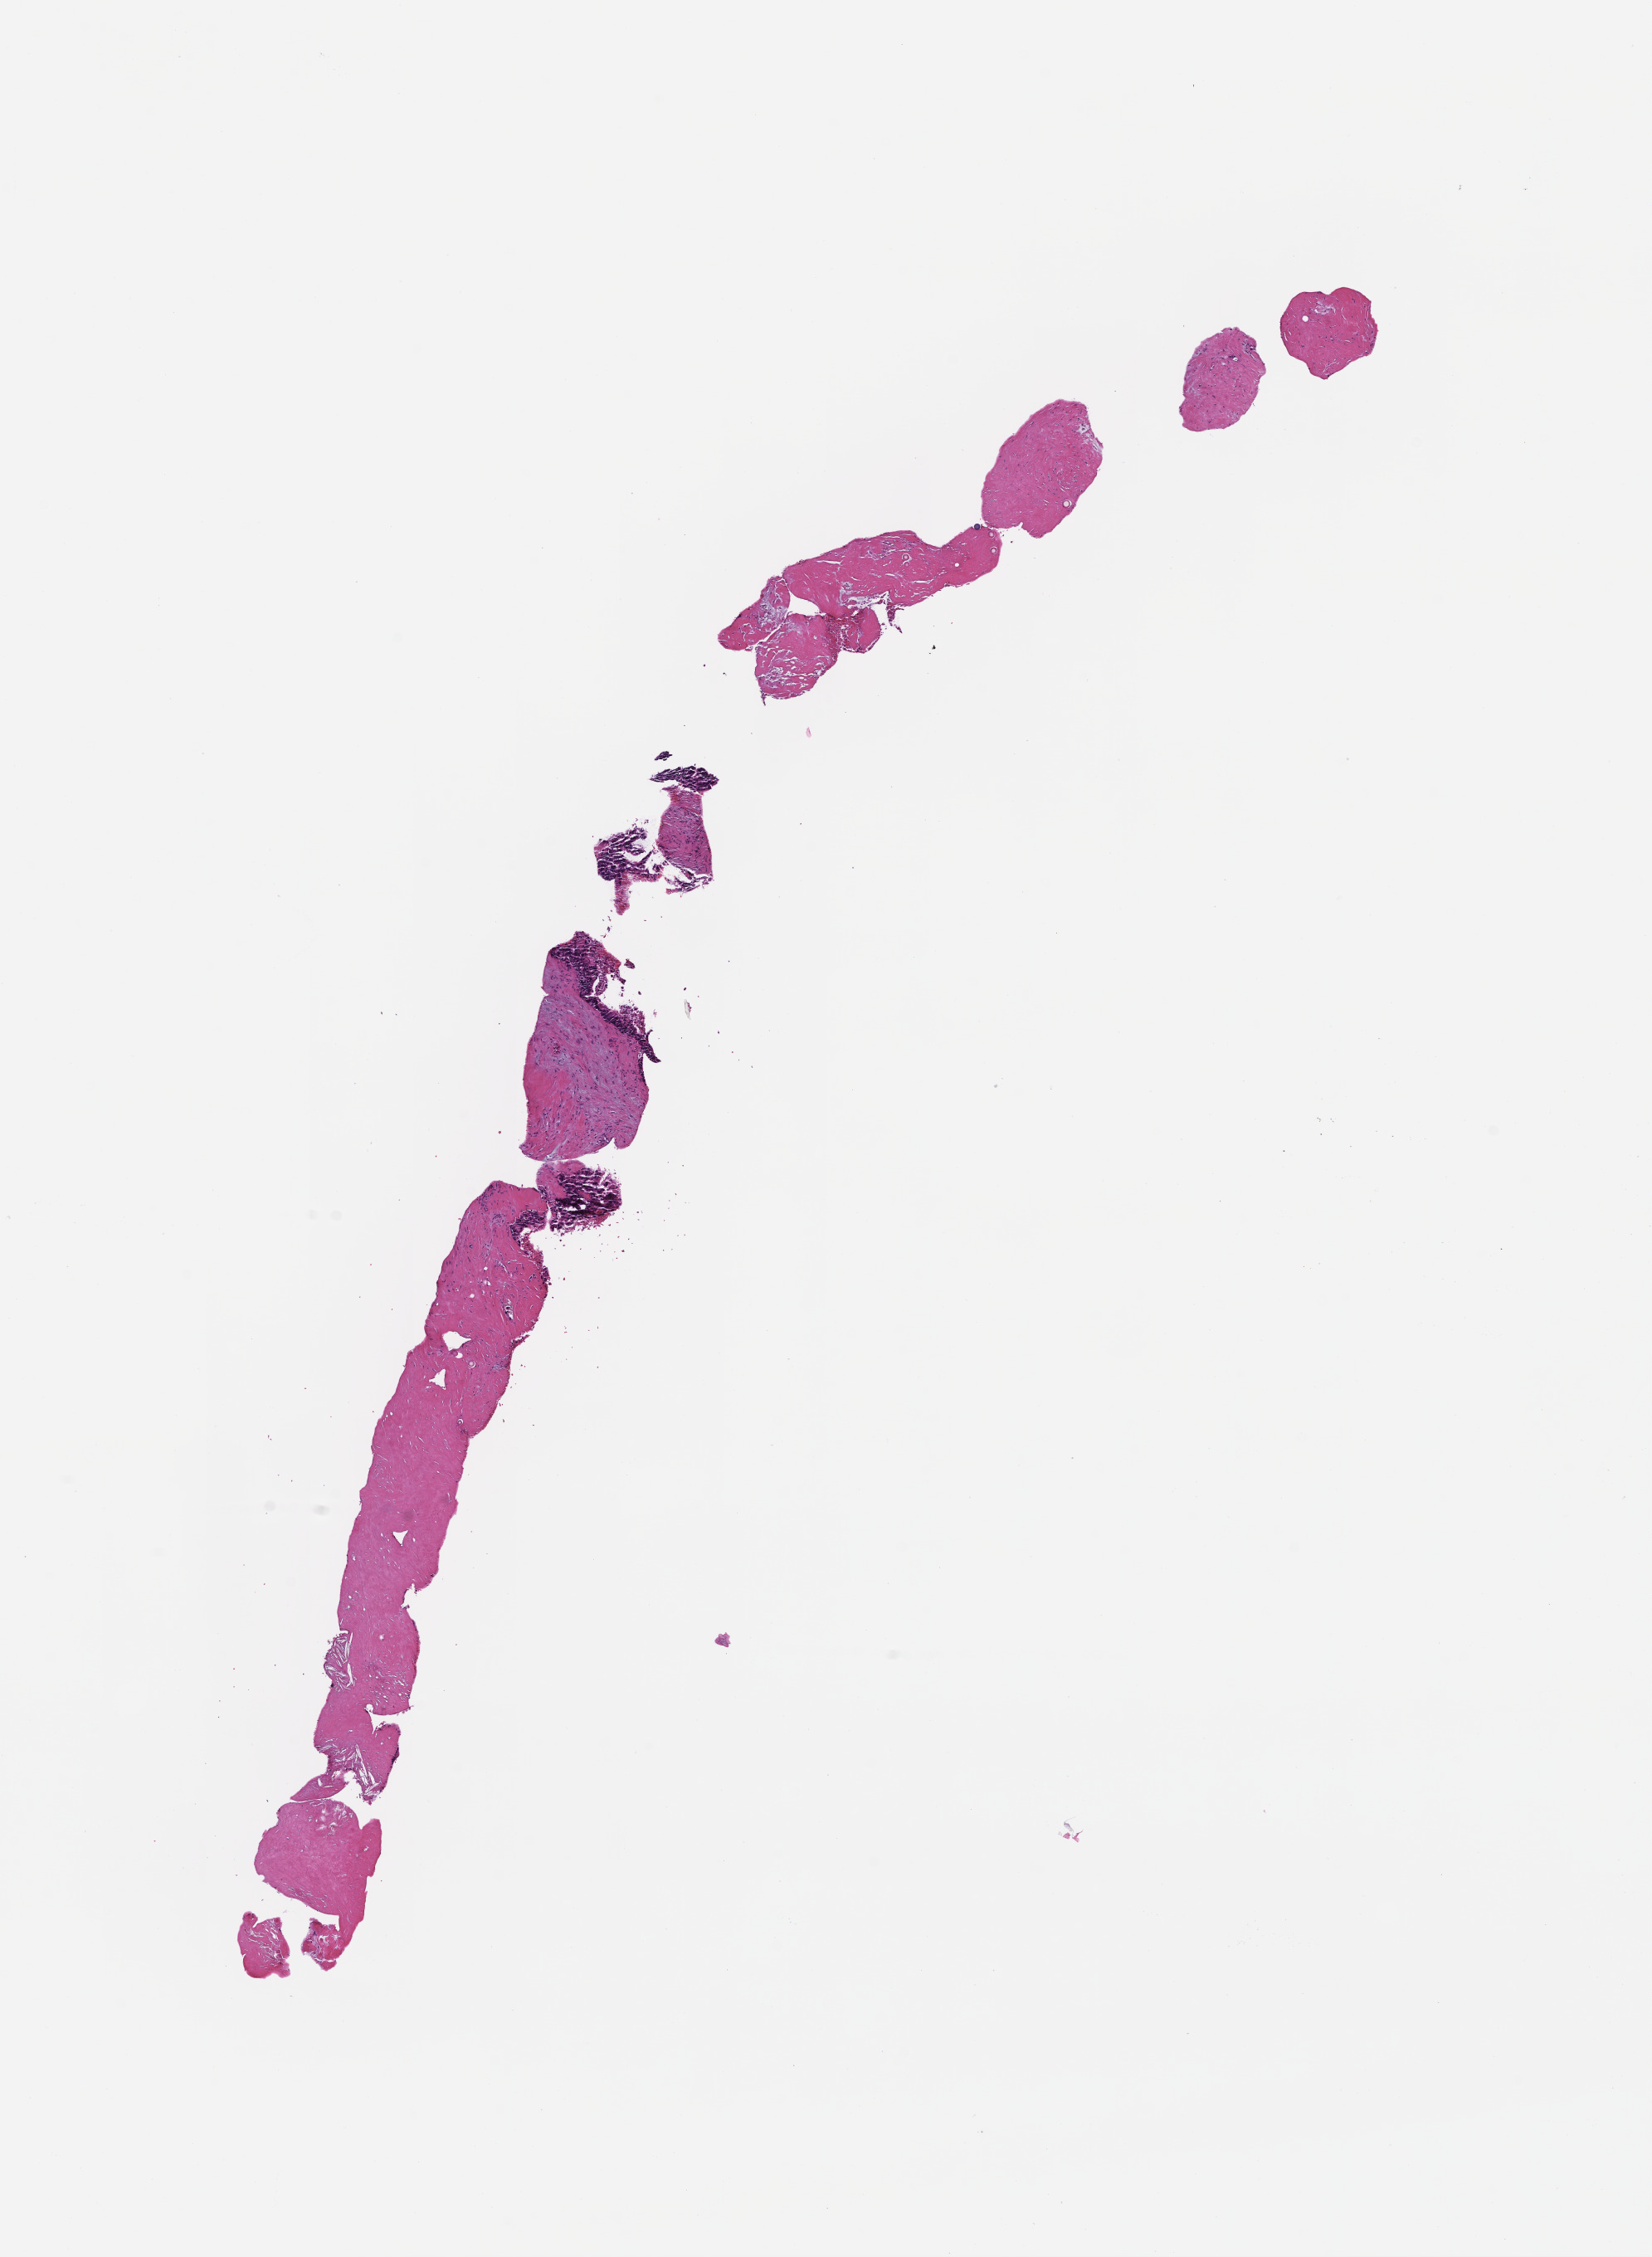
Hematoxylin and eosin (H&E) whole-slide image, a low-resolution overview of the entire scanned area, about 8.0 x 11.0 mm; FFPE section; specimen time point: collected at disease progression. Patient: male.
• this section: metastasis (sampled organ not recorded)
• patient diagnosis (primary): Colorectal Carcinoma